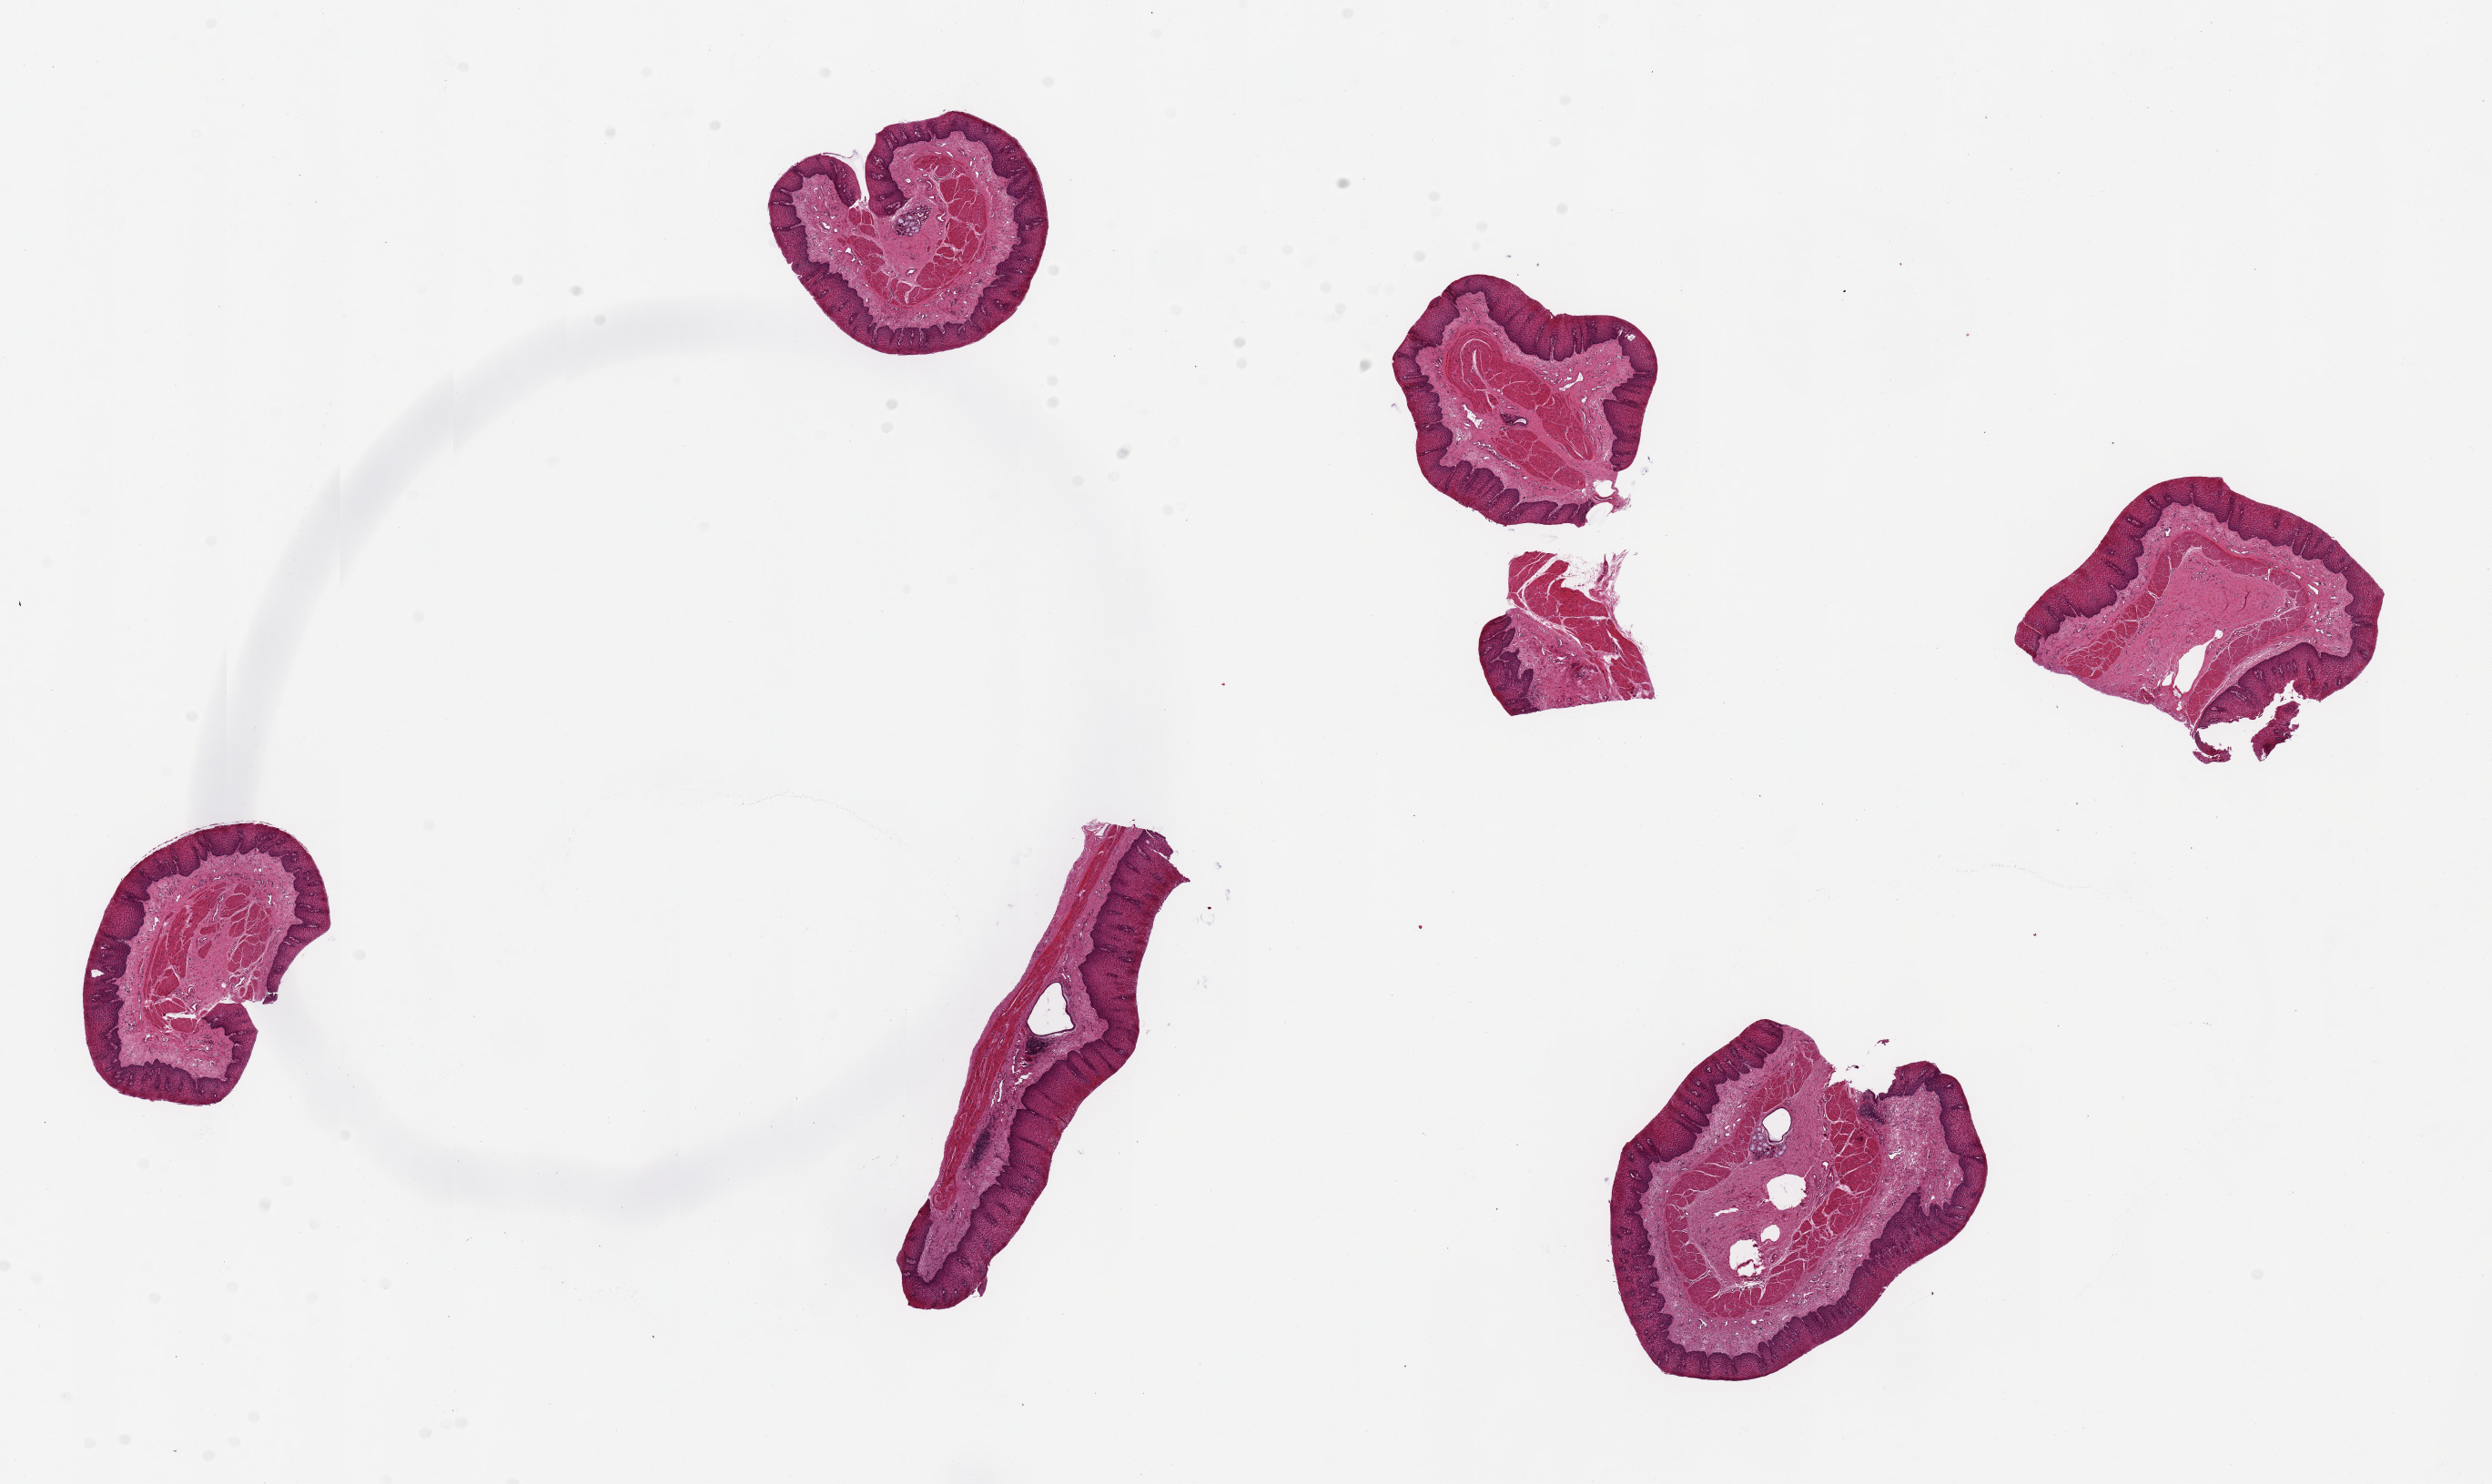
Digitized H&E-stained section, brightfield, shown as a low-resolution overview of the whole scanned area (about 21.7 x 12.9 mm, from a 20x scan). PAXgene-fixed, paraffin-embedded tissue. Section of esophageal mucous membrane (target tissue). Tissue donor sample. Donor: female.
• pathologist's review note for this sample: 6 pieces up to 4x1 mm; thickened mucosa with epithelium up to 0.5 mm; well preserved